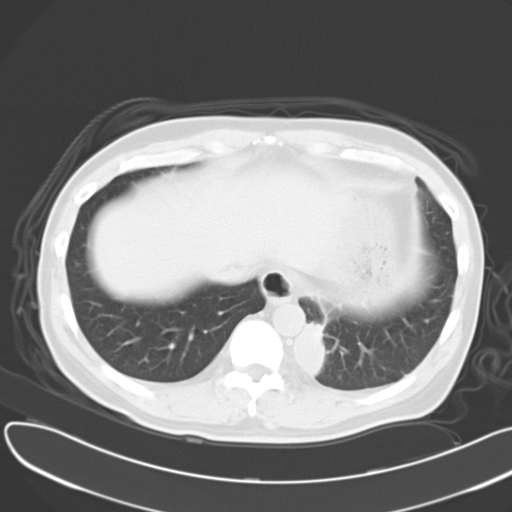
Chest CT, one axial slice. Slice 8 of 30 in the series (ordered by position). 120 kVp. Lung window (W 1500 / L -600 HU). 10 mm slice thickness. 512 × 512 image matrix, field of view 376 × 376 mm. Patient: male, 55 years. From the clinical record (not read from this slice): clinical TNM (as recorded): T2 N3 M0.
Structures marked on this image (bounding box drawn by a radiologist):
- lung tumour (recorded histology: small cell carcinoma): box from (x=288, y=318) to (x=335, y=380) px